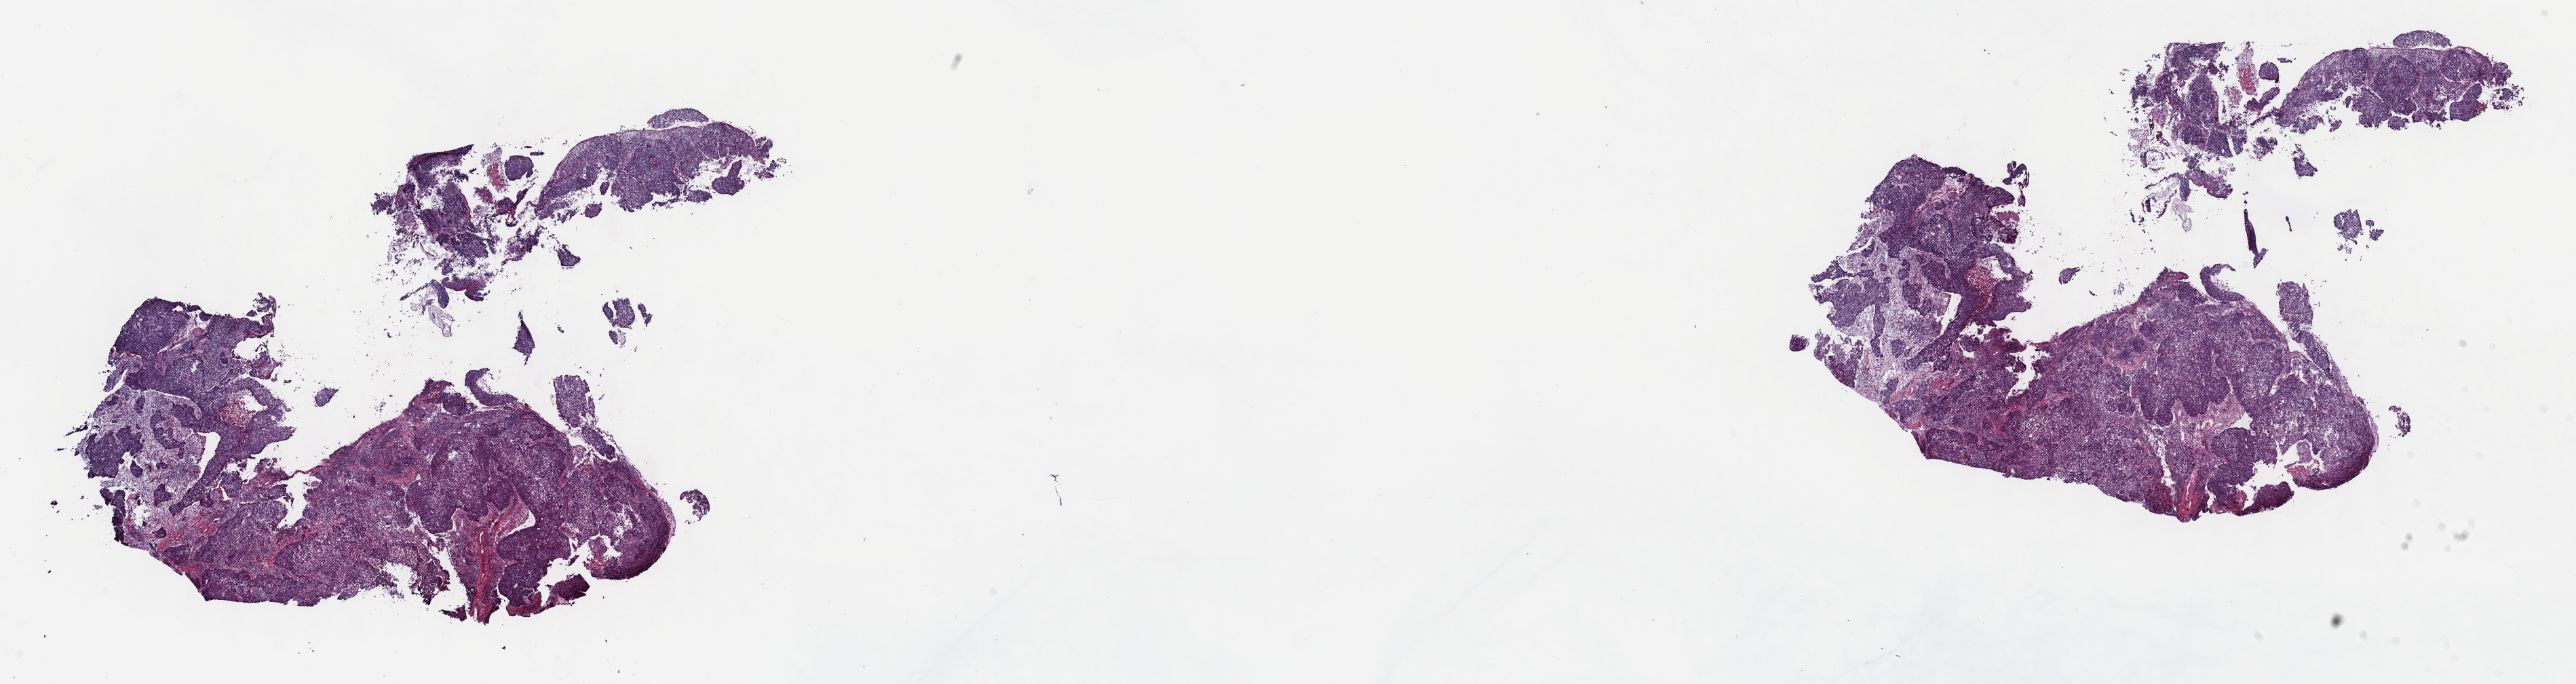
Whole-slide histology image, Hematoxylin and eosin (H&E) stained — a low-resolution overview of the entire scanned area, about 30.7 x 8.2 mm. Frozen section from the top of the tissue portion. Primary tumour sample from the cervix. Female patient; age at initial diagnosis 85 years. Histologic grade: G3 (poorly differentiated). Pathologist review of this section (percent, as recorded): tumour cells 70%, tumour nuclei 70%, normal cells 5%, stromal cells 24%, necrosis 1%. Infiltration values recorded for this section: lymphocyte infiltration 10%, monocyte infiltration 0%, neutrophil infiltration 0%.
* FIGO stage: II
* lymph nodes positive (case pathology): 0 of 26 examined
* diagnosis: Squamous cell carcinoma, large cell, nonkeratinizing, NOS (cervix uteri)